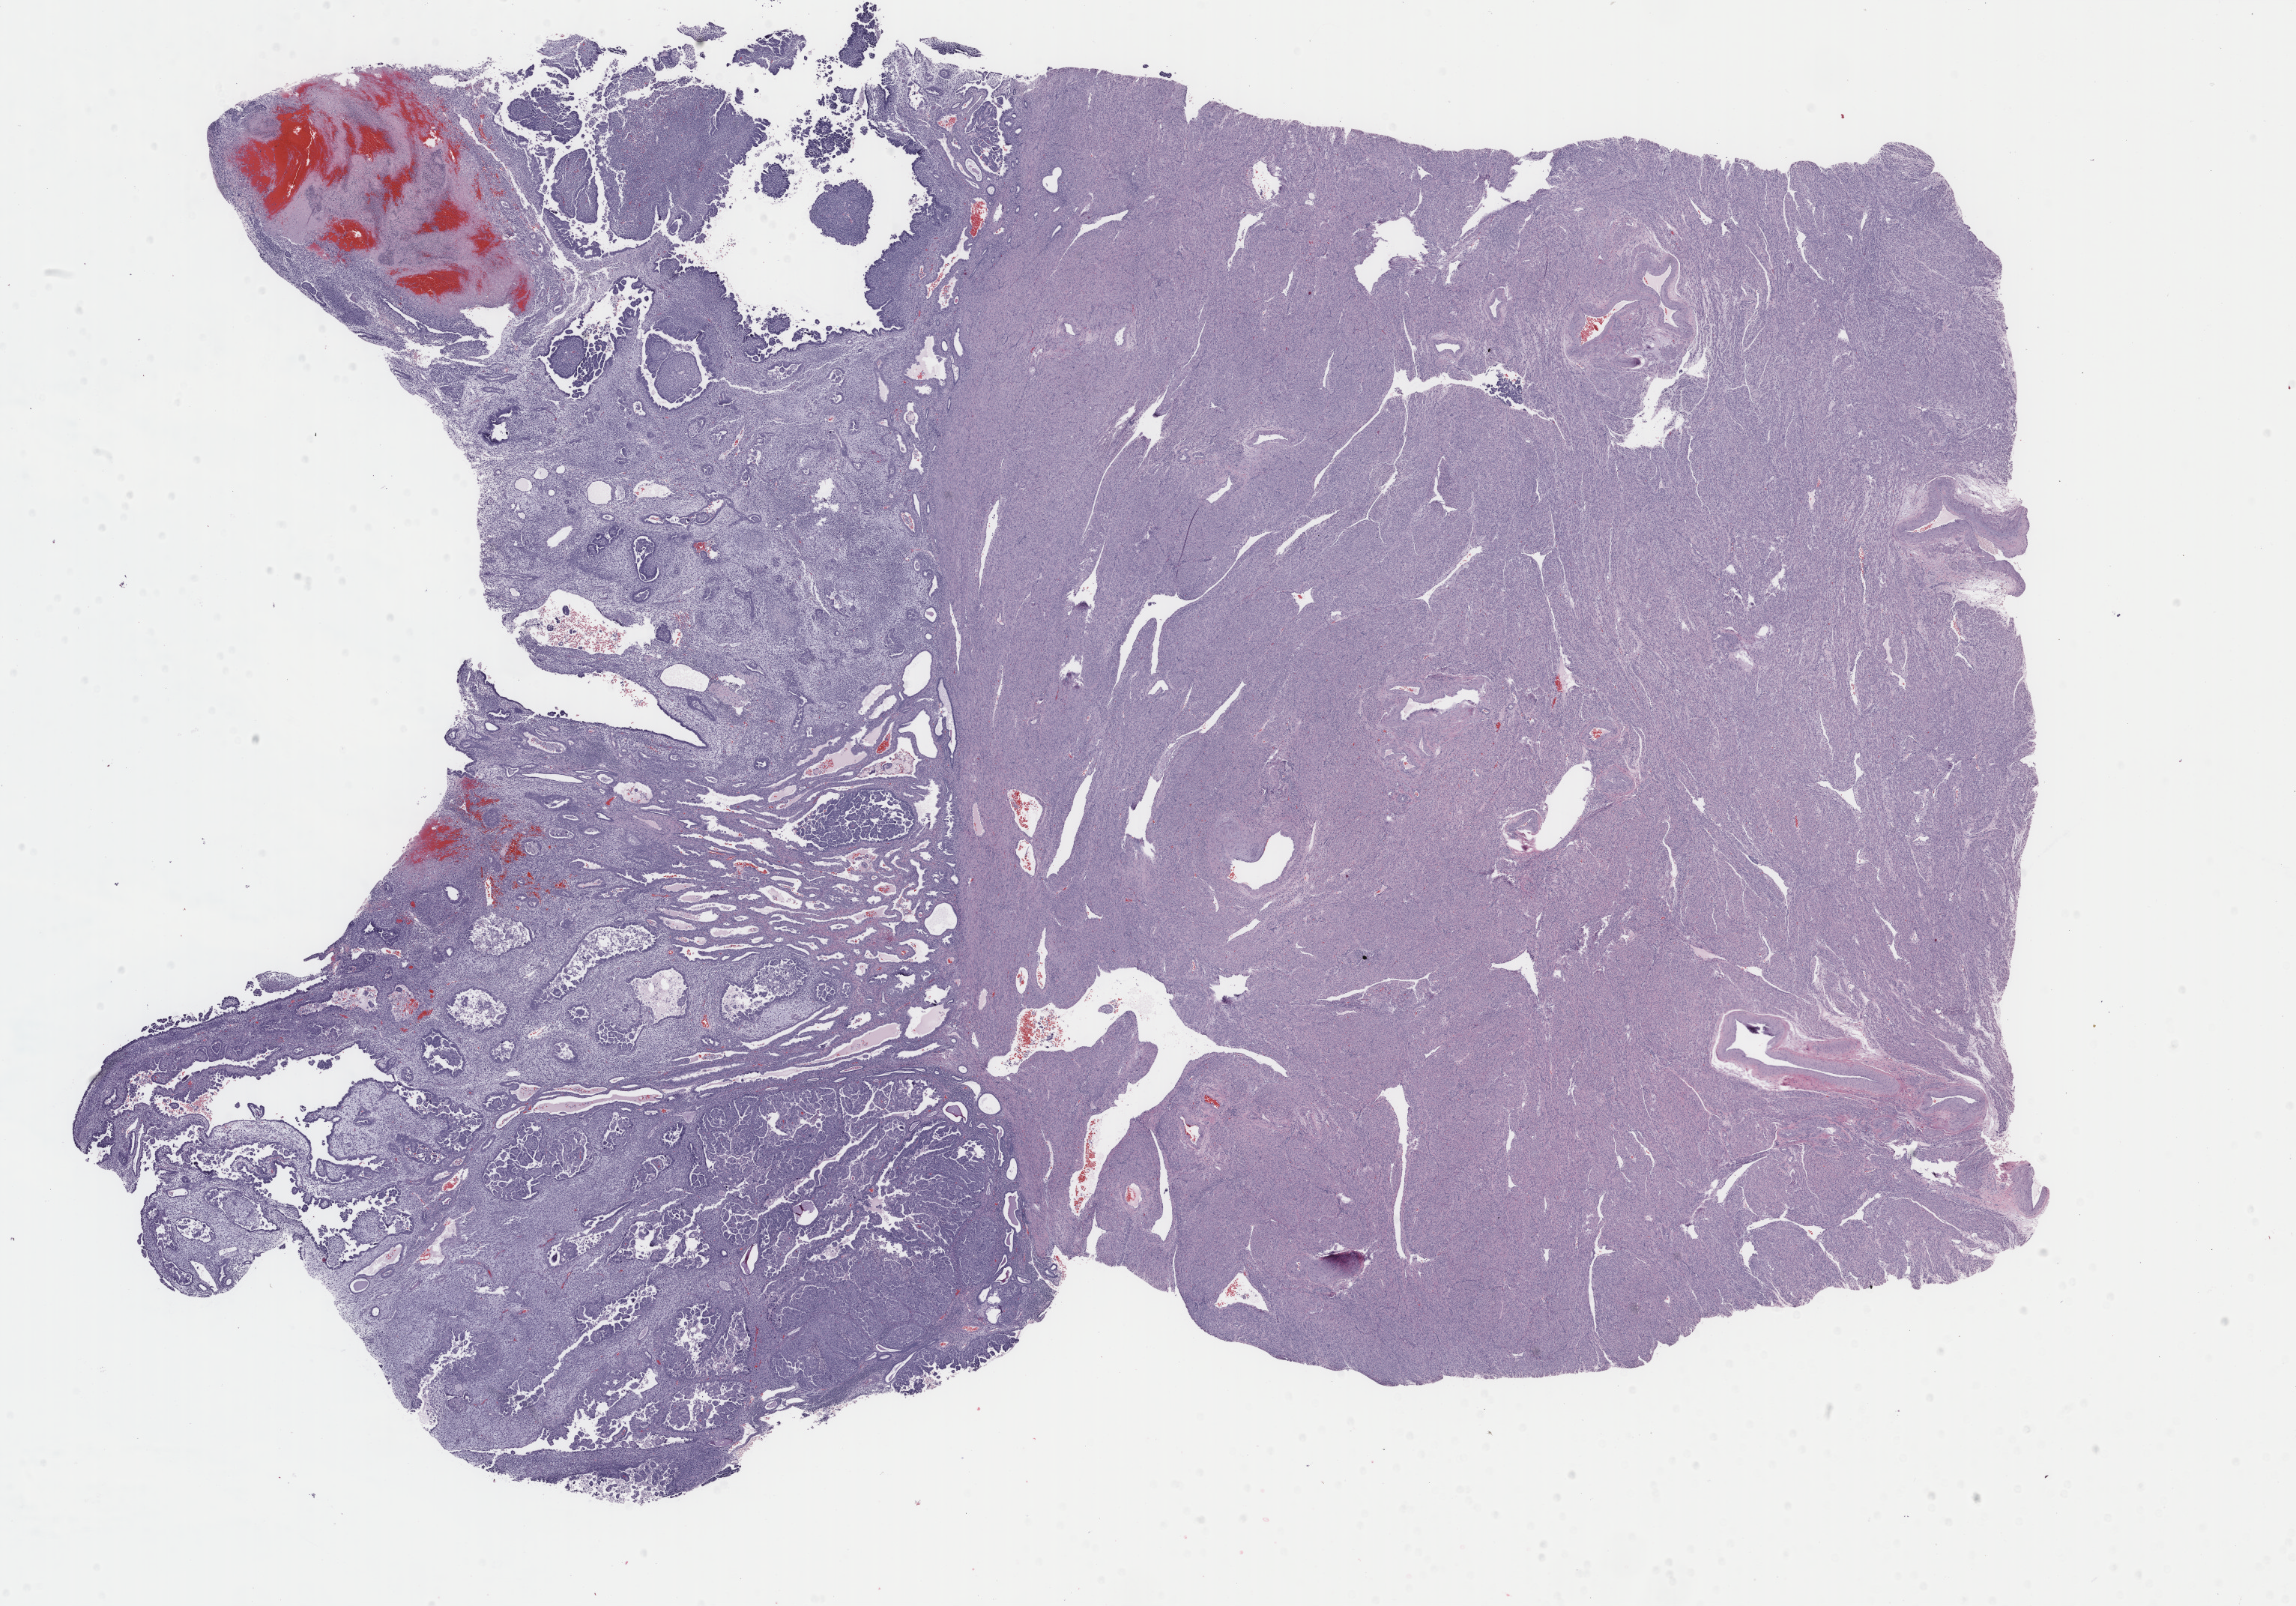
Whole-slide histology image, Hematoxylin and eosin (H&E) stained, whole scanned area (about 24.3 x 17.0 mm, acquisition: 40x scan) shown as a low-resolution overview, formalin-fixed paraffin-embedded (FFPE) diagnostic section, uterus, primary tumour sample. Female patient; age at initial diagnosis 54 years.
Lymph nodes positive (case pathology): 0 of 1 examined. FIGO stage: IIIC2. Diagnosis: Mullerian mixed tumor (endometrium).